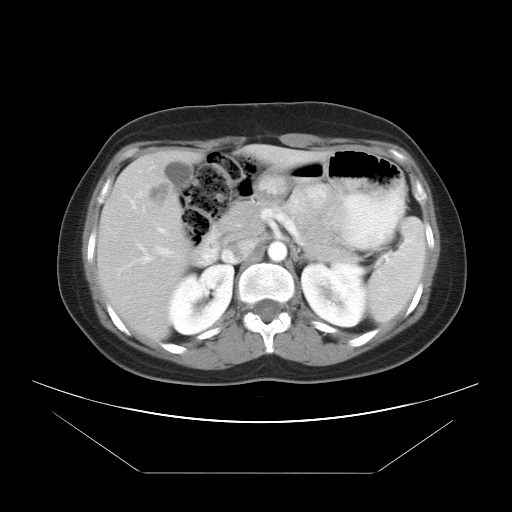
Contrast-enhanced abdominal CT, one axial slice. Slice 22 of 34 in the series (ordered by position). Reconstruction kernel STANDARD. Intravenous contrast given. Soft-tissue window (W 400 / L 40 HU). 512 × 512 image matrix. Female patient, age 38 years. From the clinical record (not read from this slice): diagnosis: colorectal cancer liver metastases, imaged before liver resection; multiple liver metastases: yes; largest metastasis: 3.1 cm.
Outlined on this slice (manually delineated by an expert):
- liver: box from (x=97, y=149) to (x=318, y=338) px
- planned liver remnant (the part of the liver to remain after resection): (x=252, y=150)–(x=323, y=160)
- portal vein (with intrahepatic branches): (x=119, y=206)–(x=216, y=271)
- liver metastasis: (x=146, y=180)–(x=174, y=207)